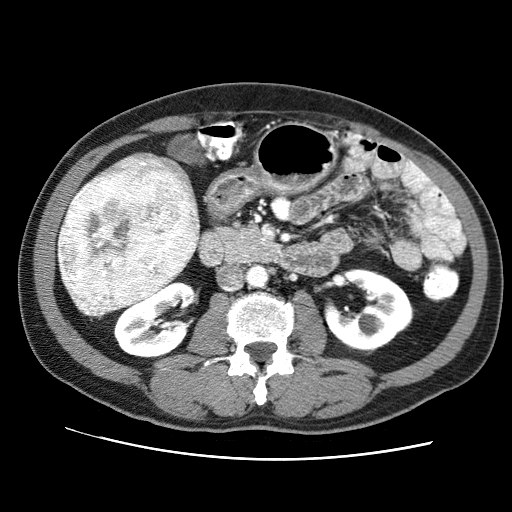
Contrast-enhanced abdominal CT (liver protocol), one axial slice. Position 24 of 71 along the scan axis. Soft-tissue window (W 400 / L 40 HU). 2.5 mm slice thickness. 512 × 512 image matrix. Case-level facts recorded for this patient, not image findings: diagnosis: hepatocellular carcinoma (patient treated with transarterial chemoembolisation; whether this scan precedes or follows treatment is not stated here); TNM stage (as recorded): Stage-II; Child-Pugh class: A.
Structures marked on this image (semi-automatically segmented with operator editing):
- liver parenchyma outside the tumour (the mass and vessels are separate outlines, so this box may not span the whole liver): bounding box (x1, y1, x2, y2) in pixels: (58, 152, 200, 311)
- mass: (57, 155, 198, 317)